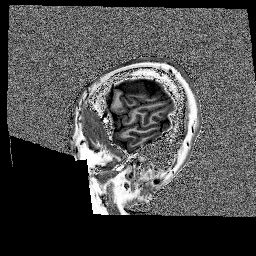
Brain MRI from a brain-tumour surgery series, one sagittal slice. 256 × 256 image matrix. Case-level facts recorded for this patient, not image findings: histopathology: Glioblastoma; WHO grade: 4; IDH mutation: no; tumour location: Left Frontal.
Structures marked on this image (manually delineated by an expert):
- tumour: bounding box (x1, y1, x2, y2) in pixels: (118, 79, 175, 98)